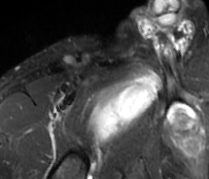
MRI of an extremity soft-tissue mass, one axial slice; slice 72 of 89 in the series (ordered by position); STIR; MR volume resampled by the dataset authors to the PET/CT grid (not the native acquisition matrix); 3.27 mm slice thickness; 209 × 179 image matrix. Male patient. From the clinical record (not read from this slice): histological type: undifferentiated - pleiomorphic; grade: high; site of the primary tumour: right thigh.
Annotated regions visible in this slice (expert contour drawn on MRI and transferred to this co-registered scan by the dataset authors):
- gross tumour volume including surrounding oedema: bounding box [x1, y1, x2, y2] px = [89, 69, 161, 143]
- gross tumour volume (mass): [89, 73, 157, 140]